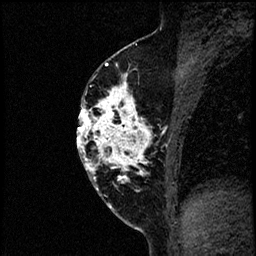
Breast MRI (dynamic contrast-enhanced), one sagittal slice; slice 34 of 60 in the series (ordered by position); dynamic contrast-enhanced study with each time point stored as its own series, time point 2 of 4 at this slice position (early post-contrast, ordered by acquisition time); 1.5 T; TE 4.2 ms, TR 17.6 ms; 2 mm slice thickness; 256 × 256 image matrix. Female patient, age 40 years. Case-level facts recorded for this patient, not image findings: setting: breast cancer imaged before/during neoadjuvant chemotherapy; receptor status: HER2-positive.
Outlined on this slice (semi-automatic segmentation, software-assisted and operator-edited):
- analysis volume of interest (the breast-tissue region the enhancement analysis was run in; not a lesion): bounding box (x1, y1, x2, y2) in pixels: (78, 56, 197, 205)
- tumour enhancement mask (voxels above the 100 % enhancement threshold inside the analysis volume of interest): (78, 63, 188, 181)